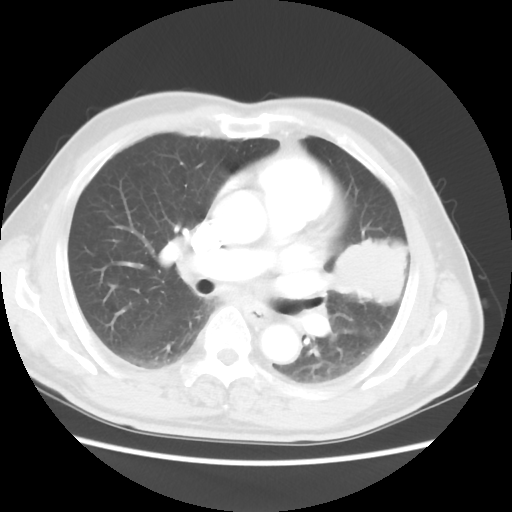
Chest CT, one axial slice; slice 28 of 50 in the series (ordered by position); reconstruction kernel STANDARD; lung window (W 1500 / L -600 HU); 5 mm slice thickness; 512 × 512 image matrix. Patient: male, 69 years. From the clinical record (not read from this slice): clinical TNM (as recorded): T3 N1 M1a.
Outlined on this slice (bounding box drawn by a radiologist):
- lung tumour (recorded histology: squamous cell carcinoma): bounding box <322,222,415,308> (left, top, right, bottom; pixels)